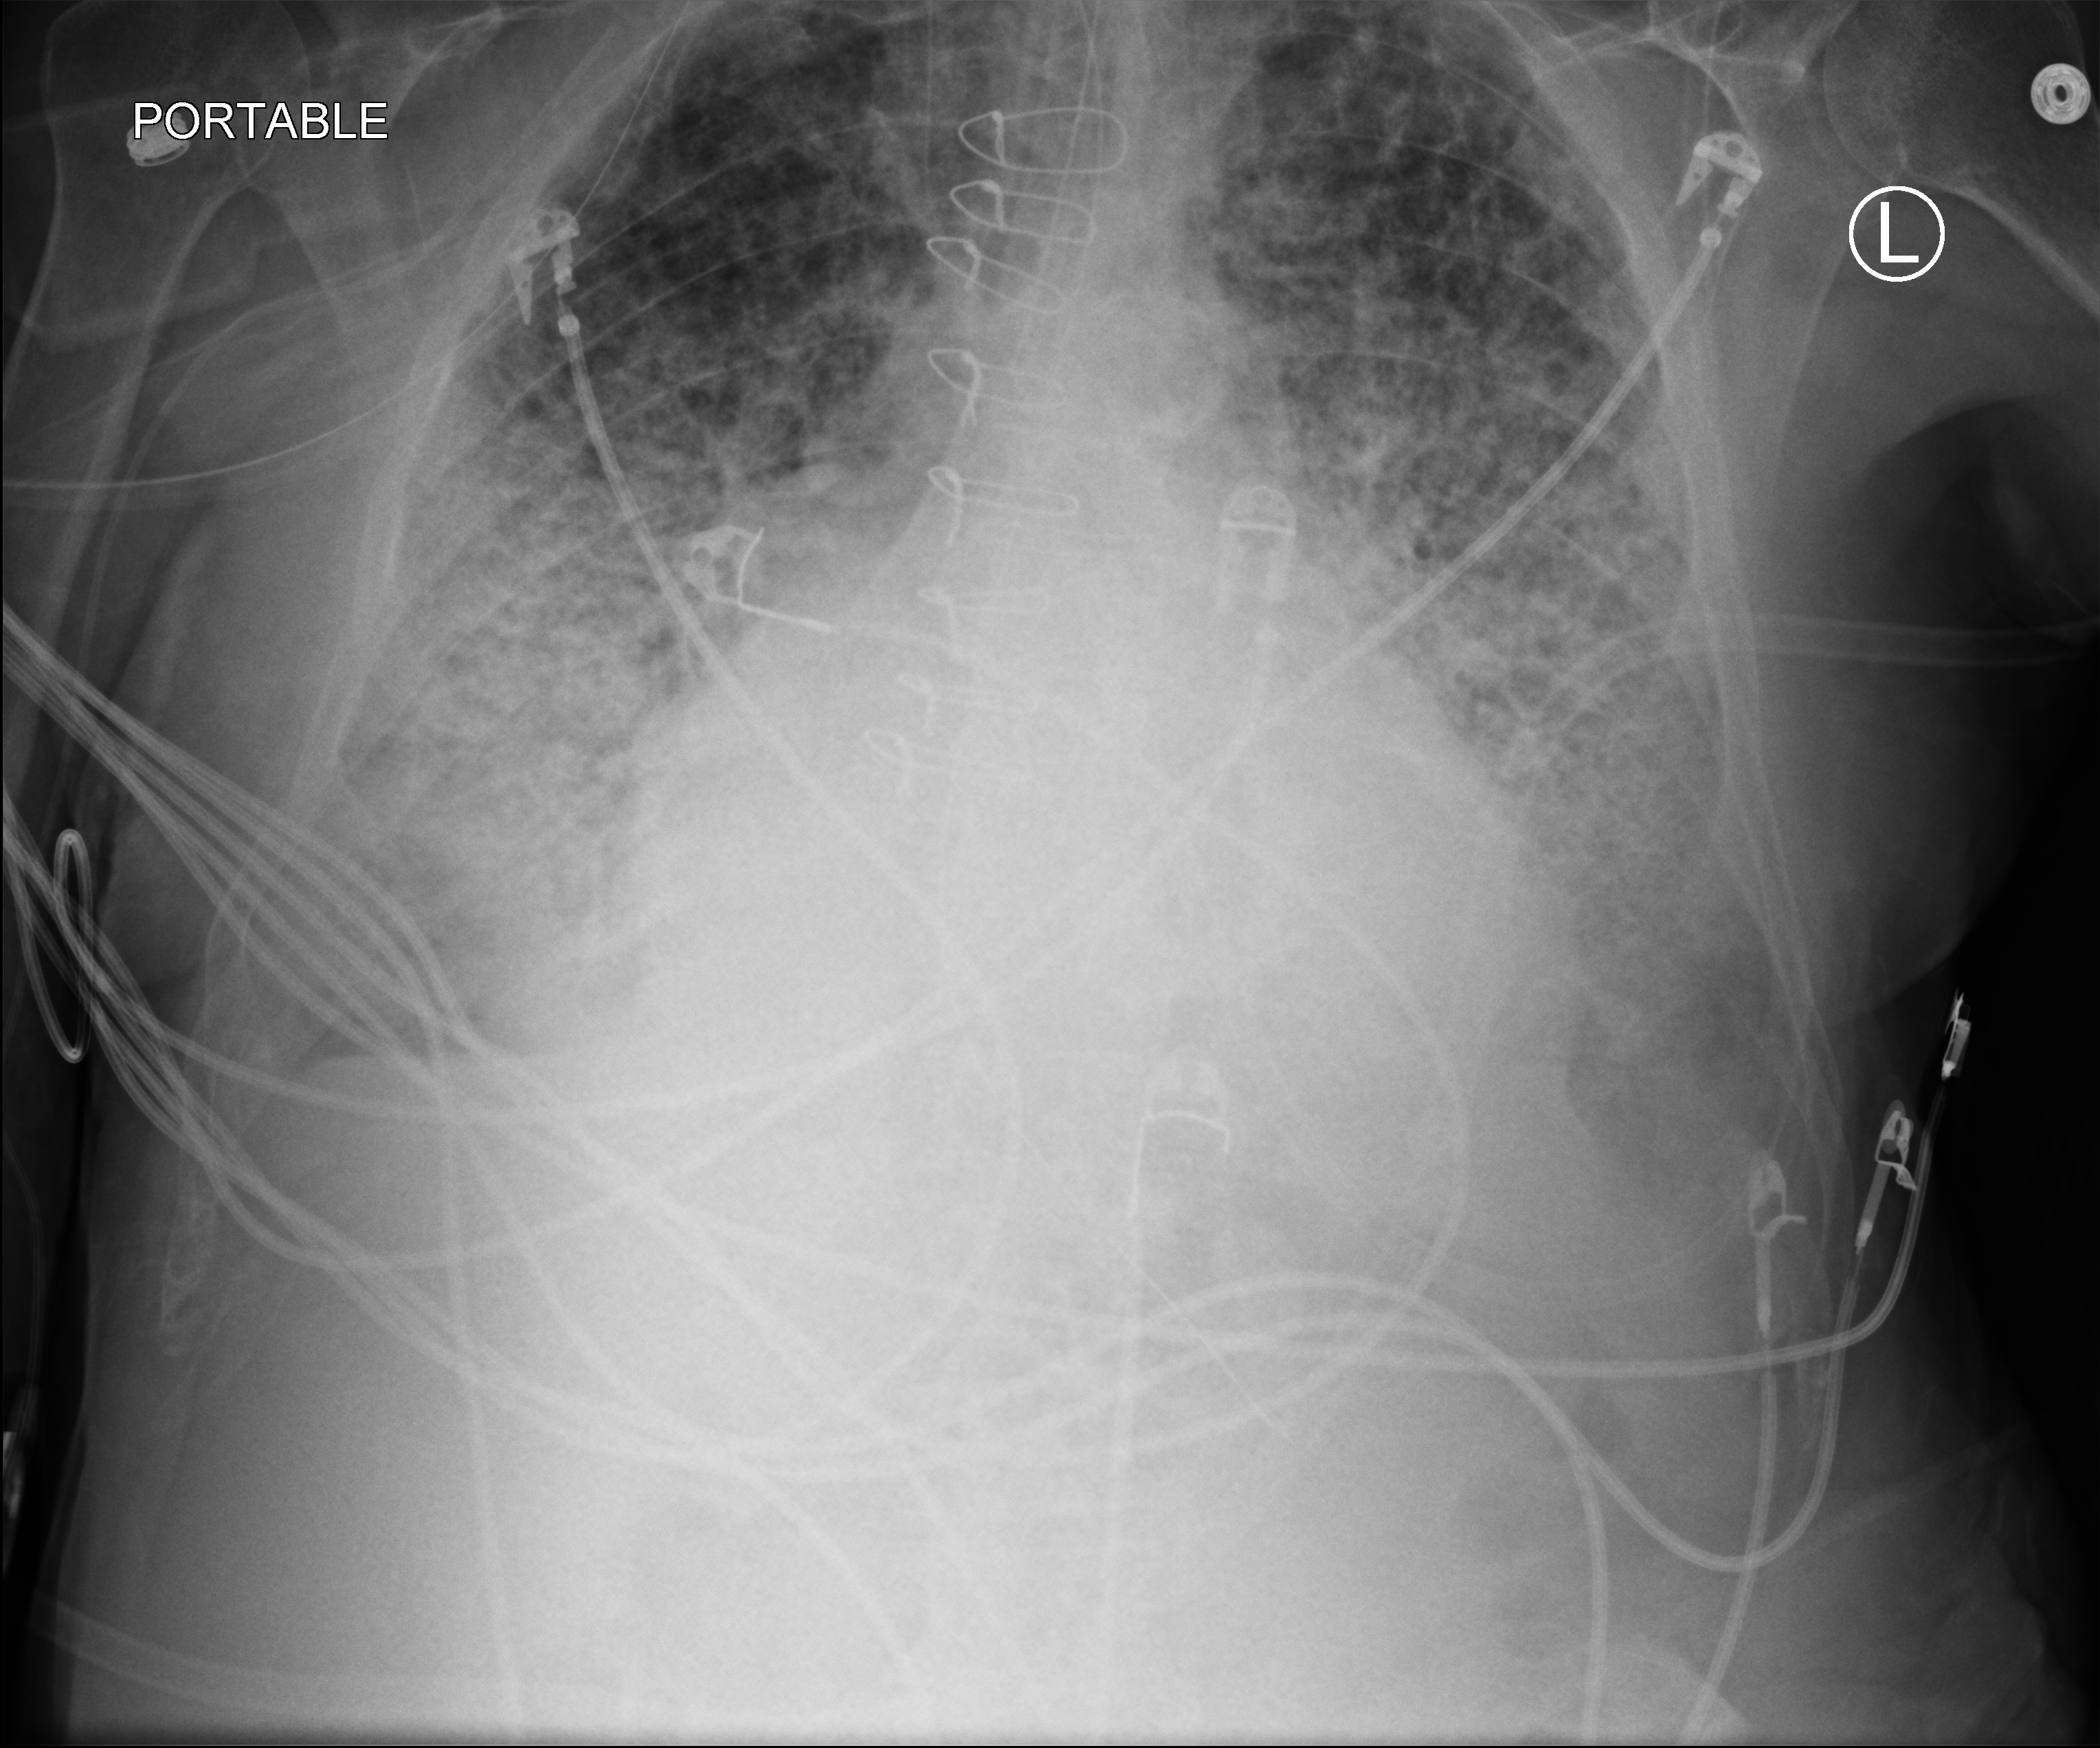
Portable chest radiograph. Patient hospitalised with COVID-19; male, aged 75–90 years.
Hospital-stay facts (about this admission, not read from this image; timing relative to this image not recorded):
- mechanically ventilated during this hospital stay: yes